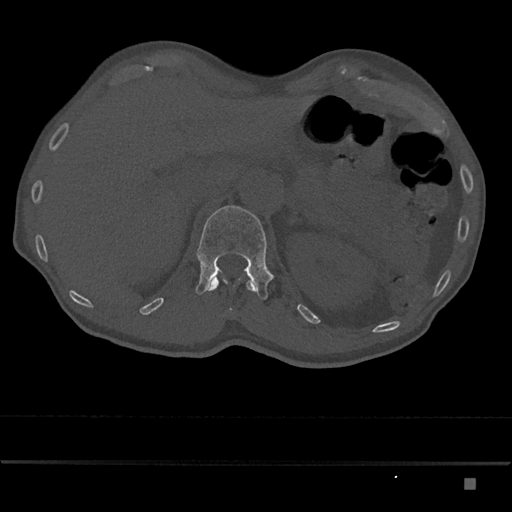
CT including the spine, one axial slice. Position 568 of 797 along the scan axis. Reconstruction kernel Br40s/3. 120 kVp. Bone window (W 1800 / L 400 HU). 0.5 mm slice thickness. 512 × 512 image matrix, field of view 390 × 390 mm. Male patient, age 72 years. From the clinical record (not read from this slice): primary cancer: prostate.
Outlined on this slice (semi-automatically segmented with operator editing):
- L1 vertebra: bounding box (x1, y1, x2, y2) in pixels: (195, 205, 275, 300)
- T12 vertebra: (206, 276, 257, 291)